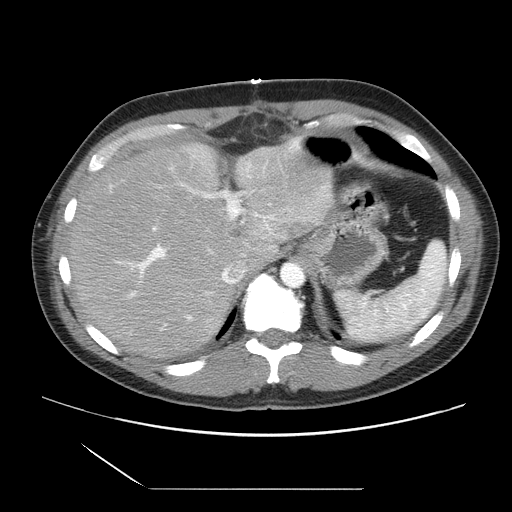
Contrast-enhanced abdominal CT, one axial slice; position 22 of 39 along the scan axis; 120 kVp; soft-tissue window (W 400 / L 40 HU); 5 mm slice thickness; 512 × 512 image matrix, field of view 395 × 395 mm. Male patient, age 39 years. From the clinical record (not read from this slice): diagnosis: colorectal cancer liver metastases, imaged before liver resection; multiple liver metastases: yes; largest metastasis: 1.3 cm; chemotherapy before resection: yes.
Outlined on this slice (expert manual segmentation):
- hepatic veins: bounding box <200,260,246,308> (left, top, right, bottom; pixels)
- liver: <71,146,332,359>
- planned liver remnant (the part of the liver to remain after resection): <112,146,332,267>
- portal vein (with intrahepatic branches): <108,162,265,332>